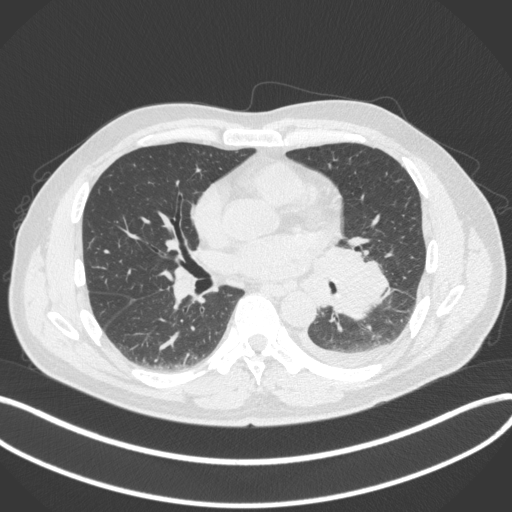
Chest CT, one axial slice. Slice 179 of 350 in the series (ordered by position). Reconstruction kernel B31f. 120 kVp. Lung window (W 1500 / L -600 HU). 1 mm slice thickness. 512 × 512 image matrix. Male patient, age 58 years. Case-level facts recorded for this patient, not image findings: clinical TNM (as recorded): T3 N1 M1b; histopathological grade: G3.
Annotated regions visible in this slice (bounding box drawn by a radiologist):
- lung tumour (recorded histology: small cell carcinoma): bounding box (x1, y1, x2, y2) in pixels: (312, 237, 392, 322)